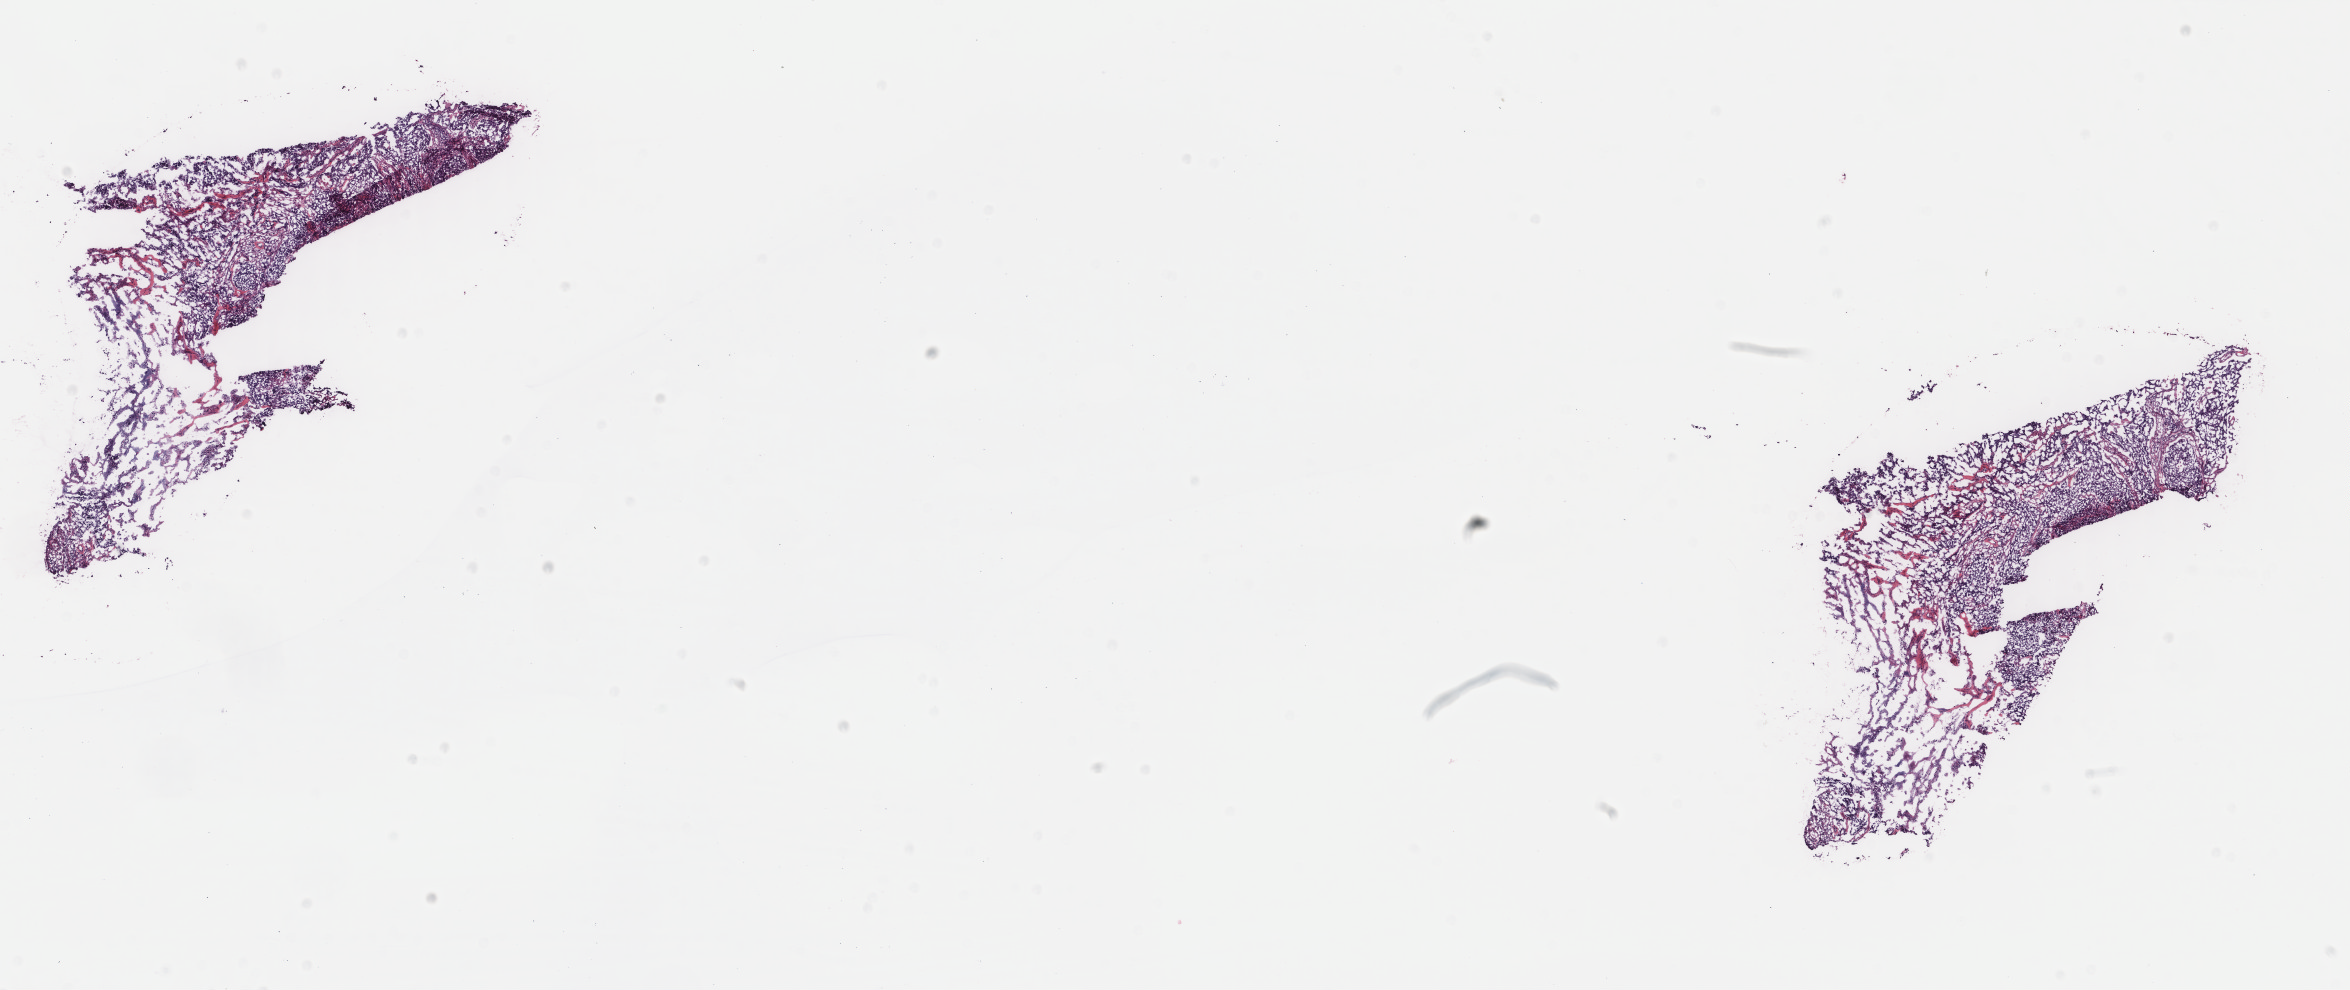
Whole-slide histology image, H&E-stained, low-resolution overview of the scanned area, about 18.7 x 7.9 mm; frozen section from the top of the tissue portion; sample: primary tumour, cervix. Female patient; age at initial diagnosis 40 years. Histologic grade: G3 (poorly differentiated). Slide review estimates, as recorded: tumour cells 75%, tumour nuclei 95%, normal cells 0%, stromal cells 20%, necrosis 5%. Inflammatory infiltration, as recorded: lymphocyte infiltration 1%, monocyte infiltration 0%, neutrophil infiltration 0%.
Pathologic diagnosis: Squamous cell carcinoma, NOS (cervix uteri). FIGO stage: IB.